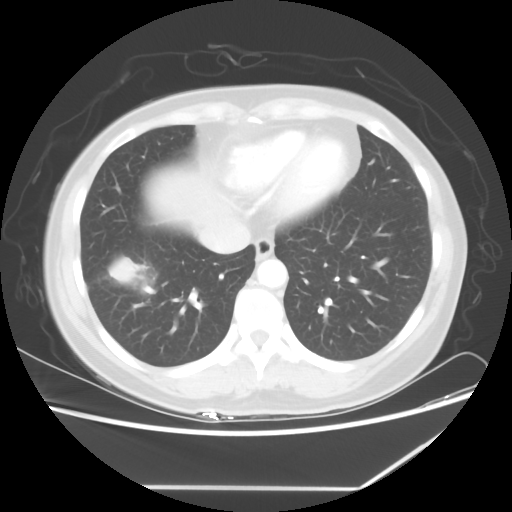
Chest CT, one axial slice. Position 20 of 60 along the scan axis. Reconstruction kernel STANDARD. 100 kVp. Lung window (W 1500 / L -600 HU). 5 mm slice thickness. 512 × 512 image matrix, field of view 374 × 374 mm. Patient: female, 42 years. Case-level facts recorded for this patient, not image findings: clinical TNM (as recorded): T2 N1 M0.
Annotated regions visible in this slice (bounding box drawn by a radiologist):
- lung tumour (recorded histology: adenocarcinoma): bounding box (x1, y1, x2, y2) in pixels: (103, 250, 139, 289)